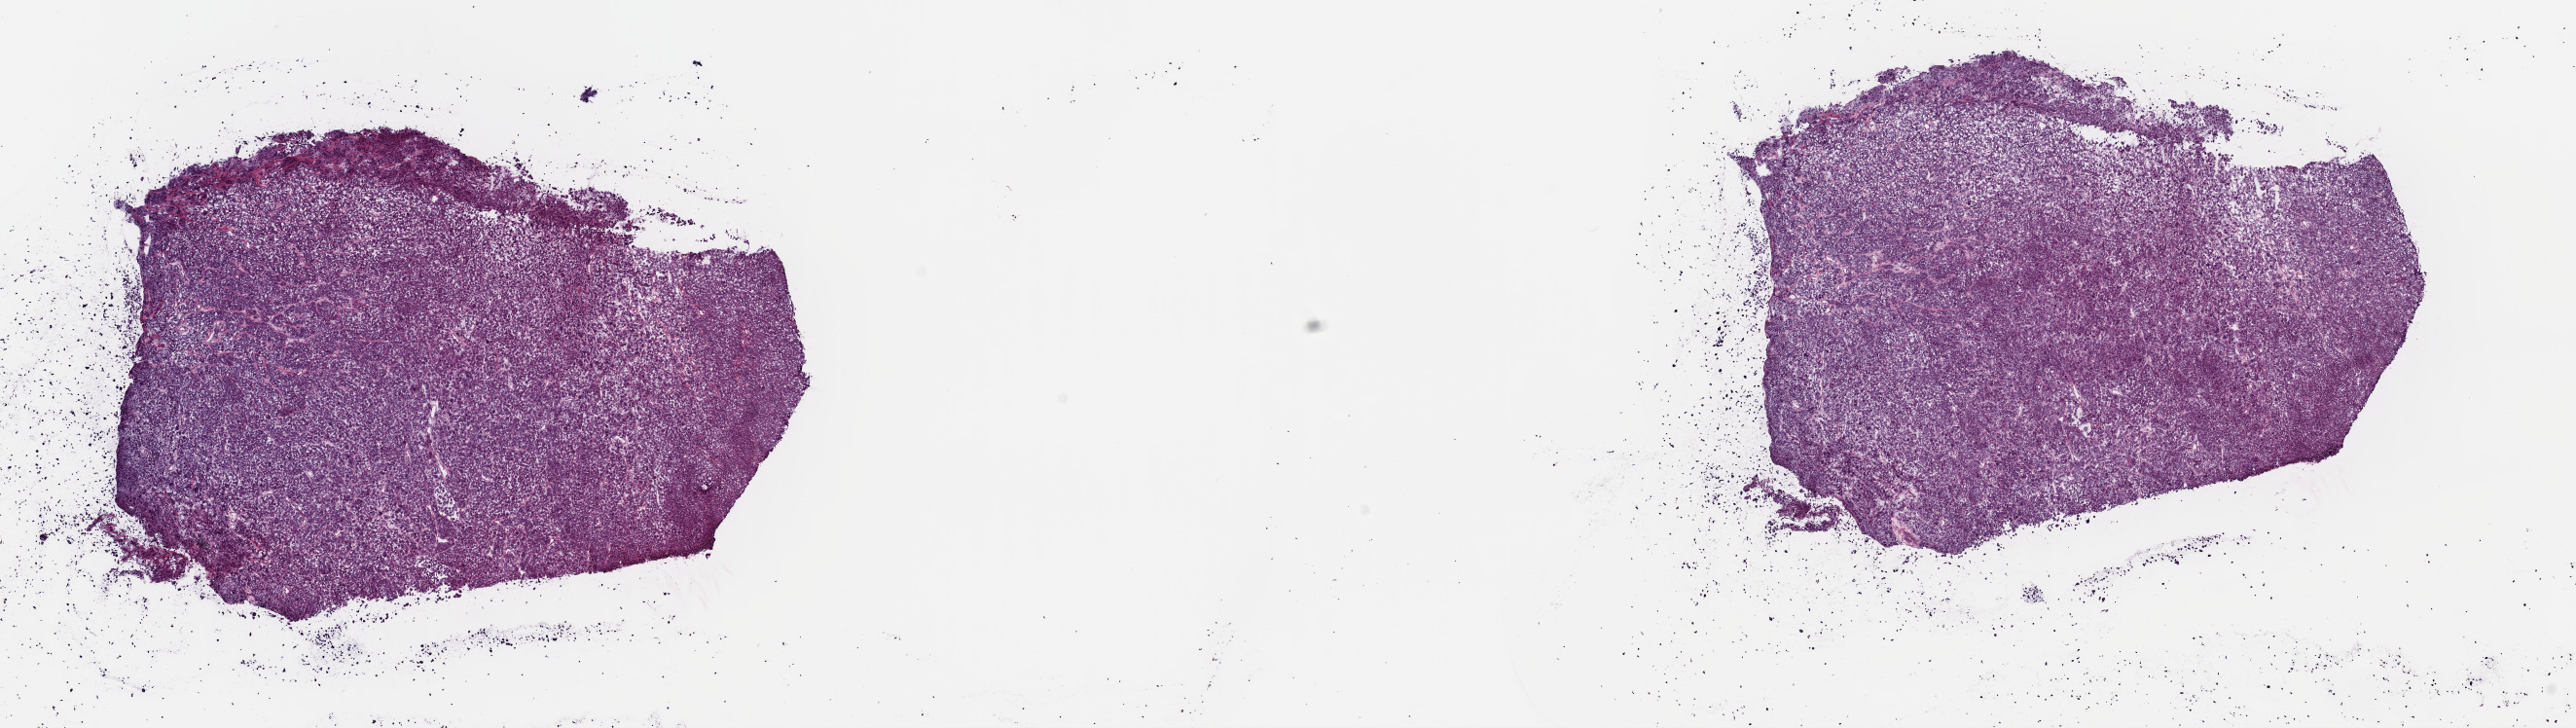
Digitized H&E-stained tissue section (whole slide) — whole scanned area (about 20.9 x 5.9 mm) shown as a low-resolution overview, frozen section from the top of the tissue portion, metastatic tumour sample. Patient: male, age at initial diagnosis 43 years. Pathologist review of this section (percent, as recorded): tumour cells 85%, tumour nuclei 85%, normal cells 0%, stromal cells 15%, necrosis 0%. Inflammatory infiltration, as recorded: lymphocyte infiltration 2%, monocyte infiltration 0%, neutrophil infiltration 0%.
This section: metastatic tumour tissue. Patient diagnosis: Malignant melanoma, NOS.